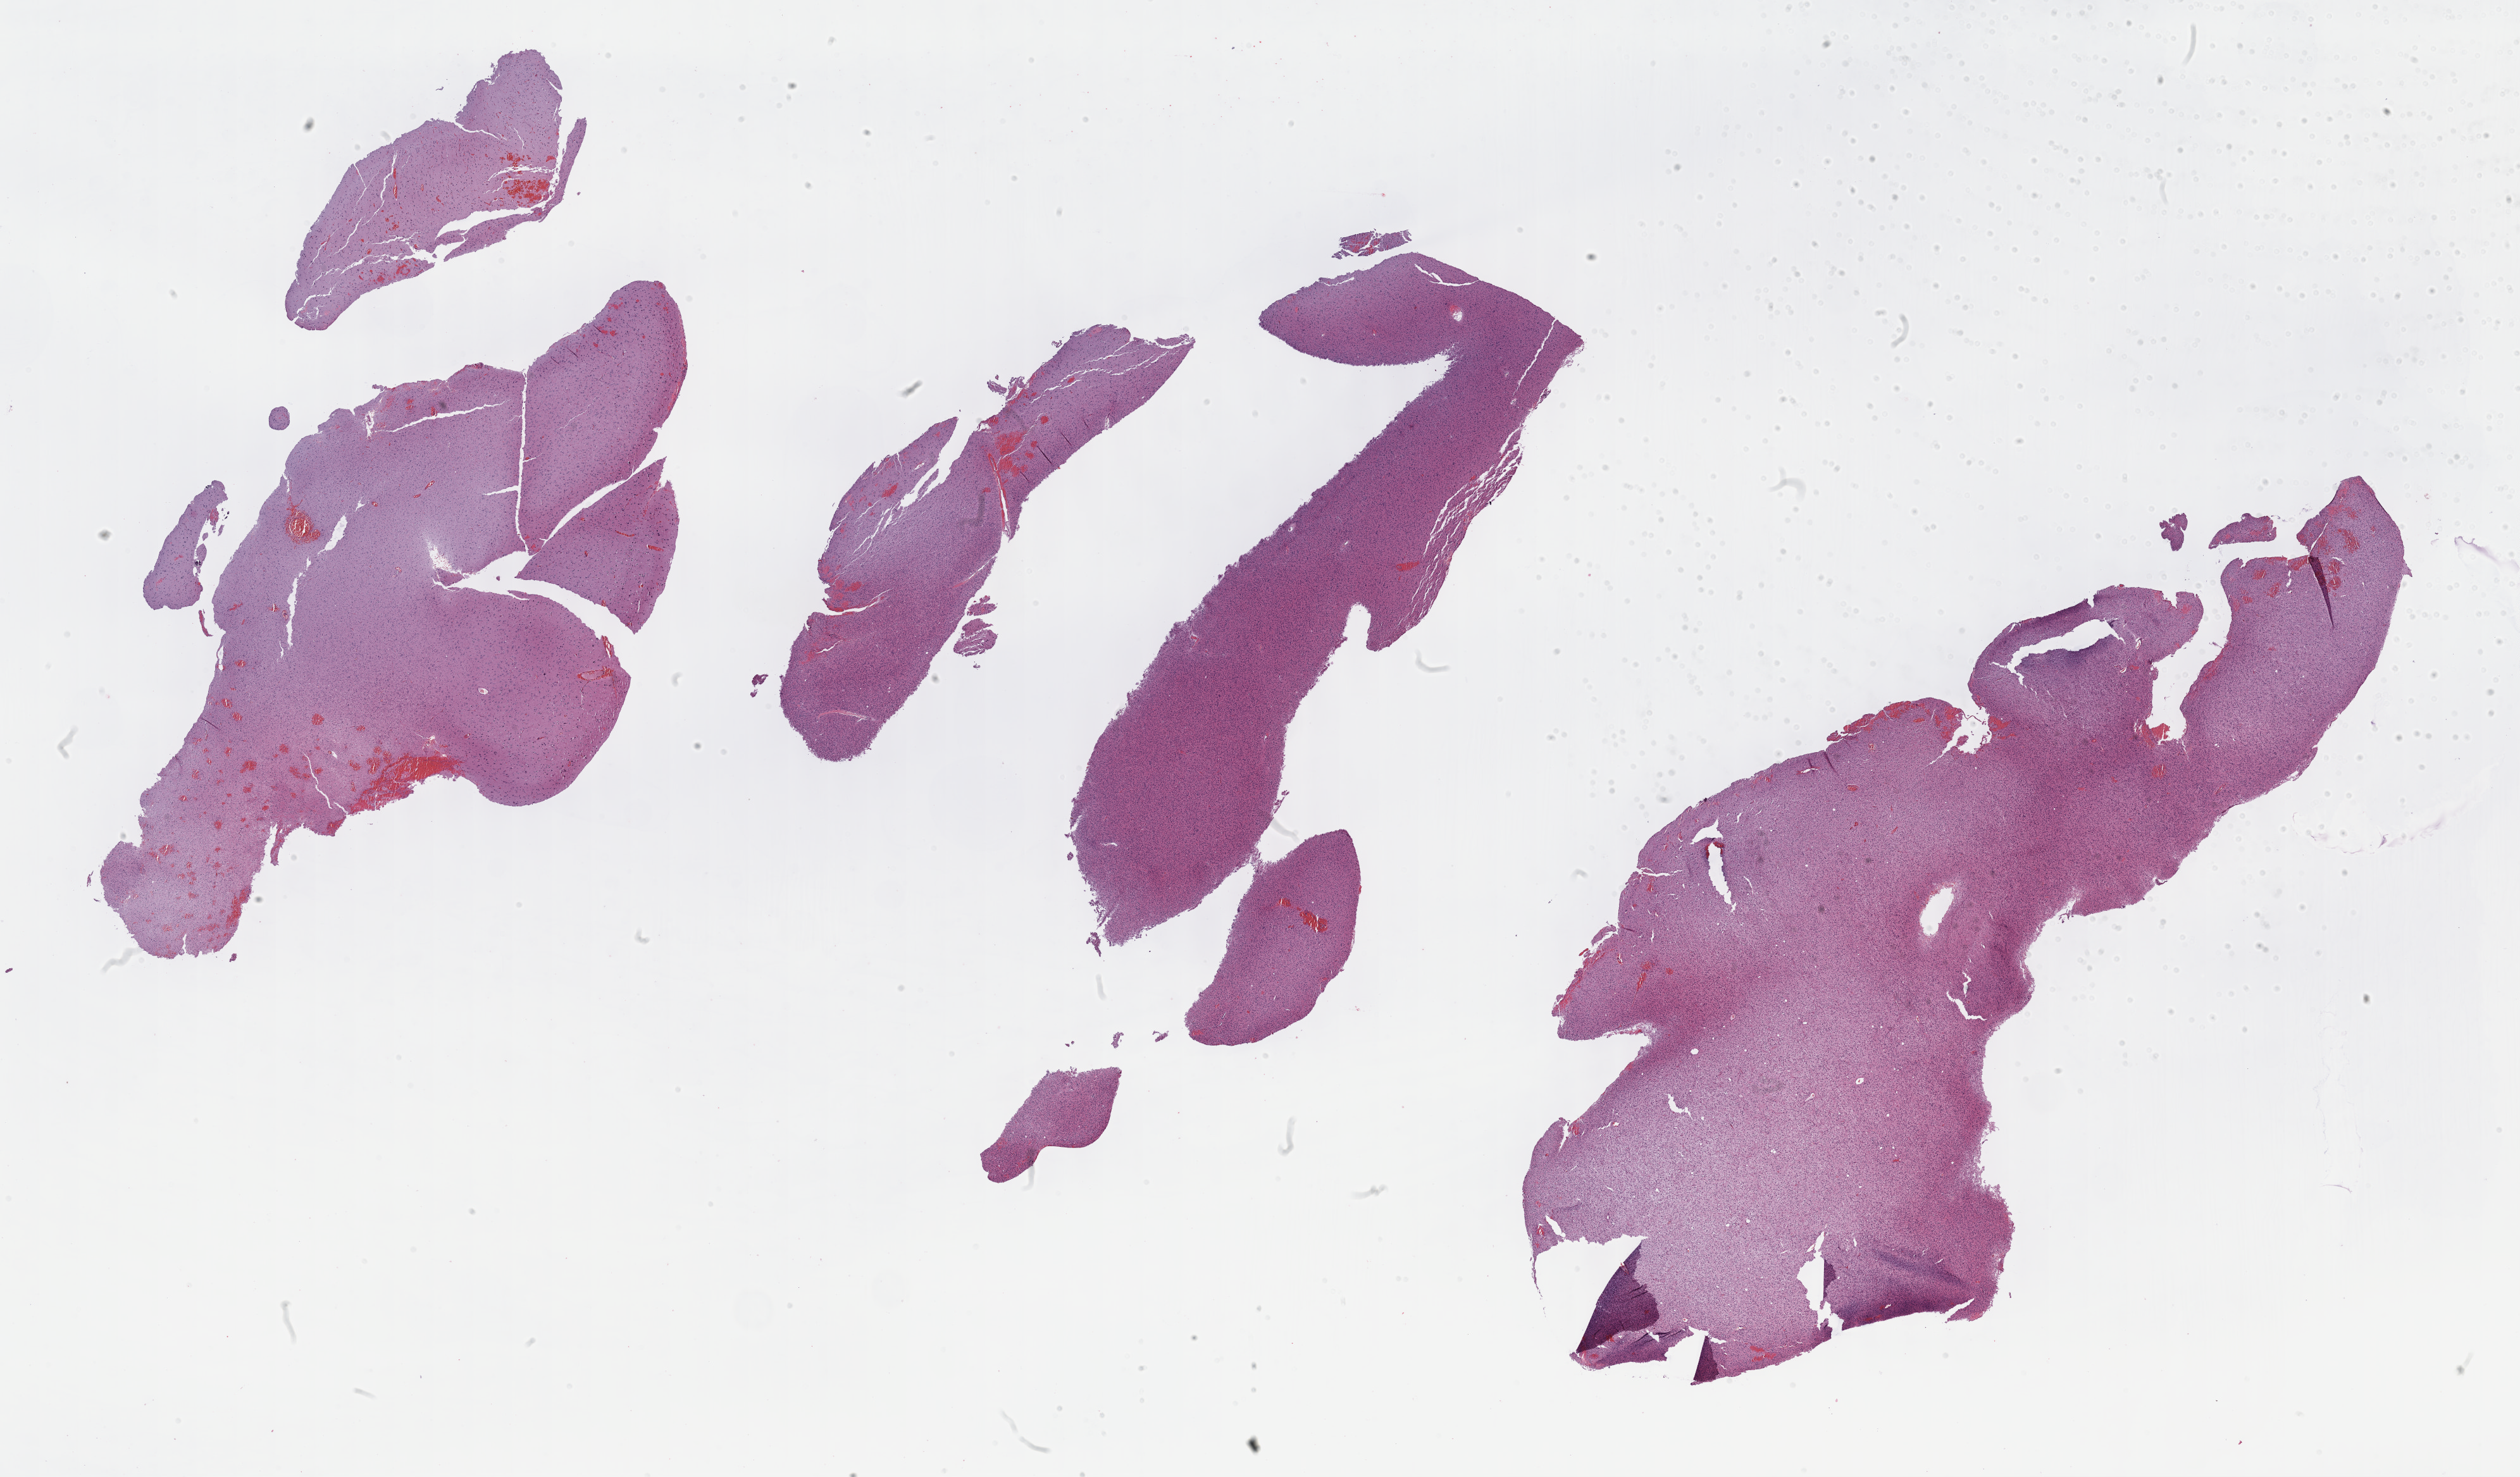
H&E whole-slide image, whole scanned area (about 32.2 x 18.9 mm, from a 40x scan) shown as a low-resolution overview, formalin-fixed paraffin-embedded (FFPE) diagnostic section, sample: primary tumour, brain. Patient: male, age at initial diagnosis 25 years. Histologic grade: G2 (moderately differentiated).
Histologic diagnosis: Oligodendroglioma, NOS.